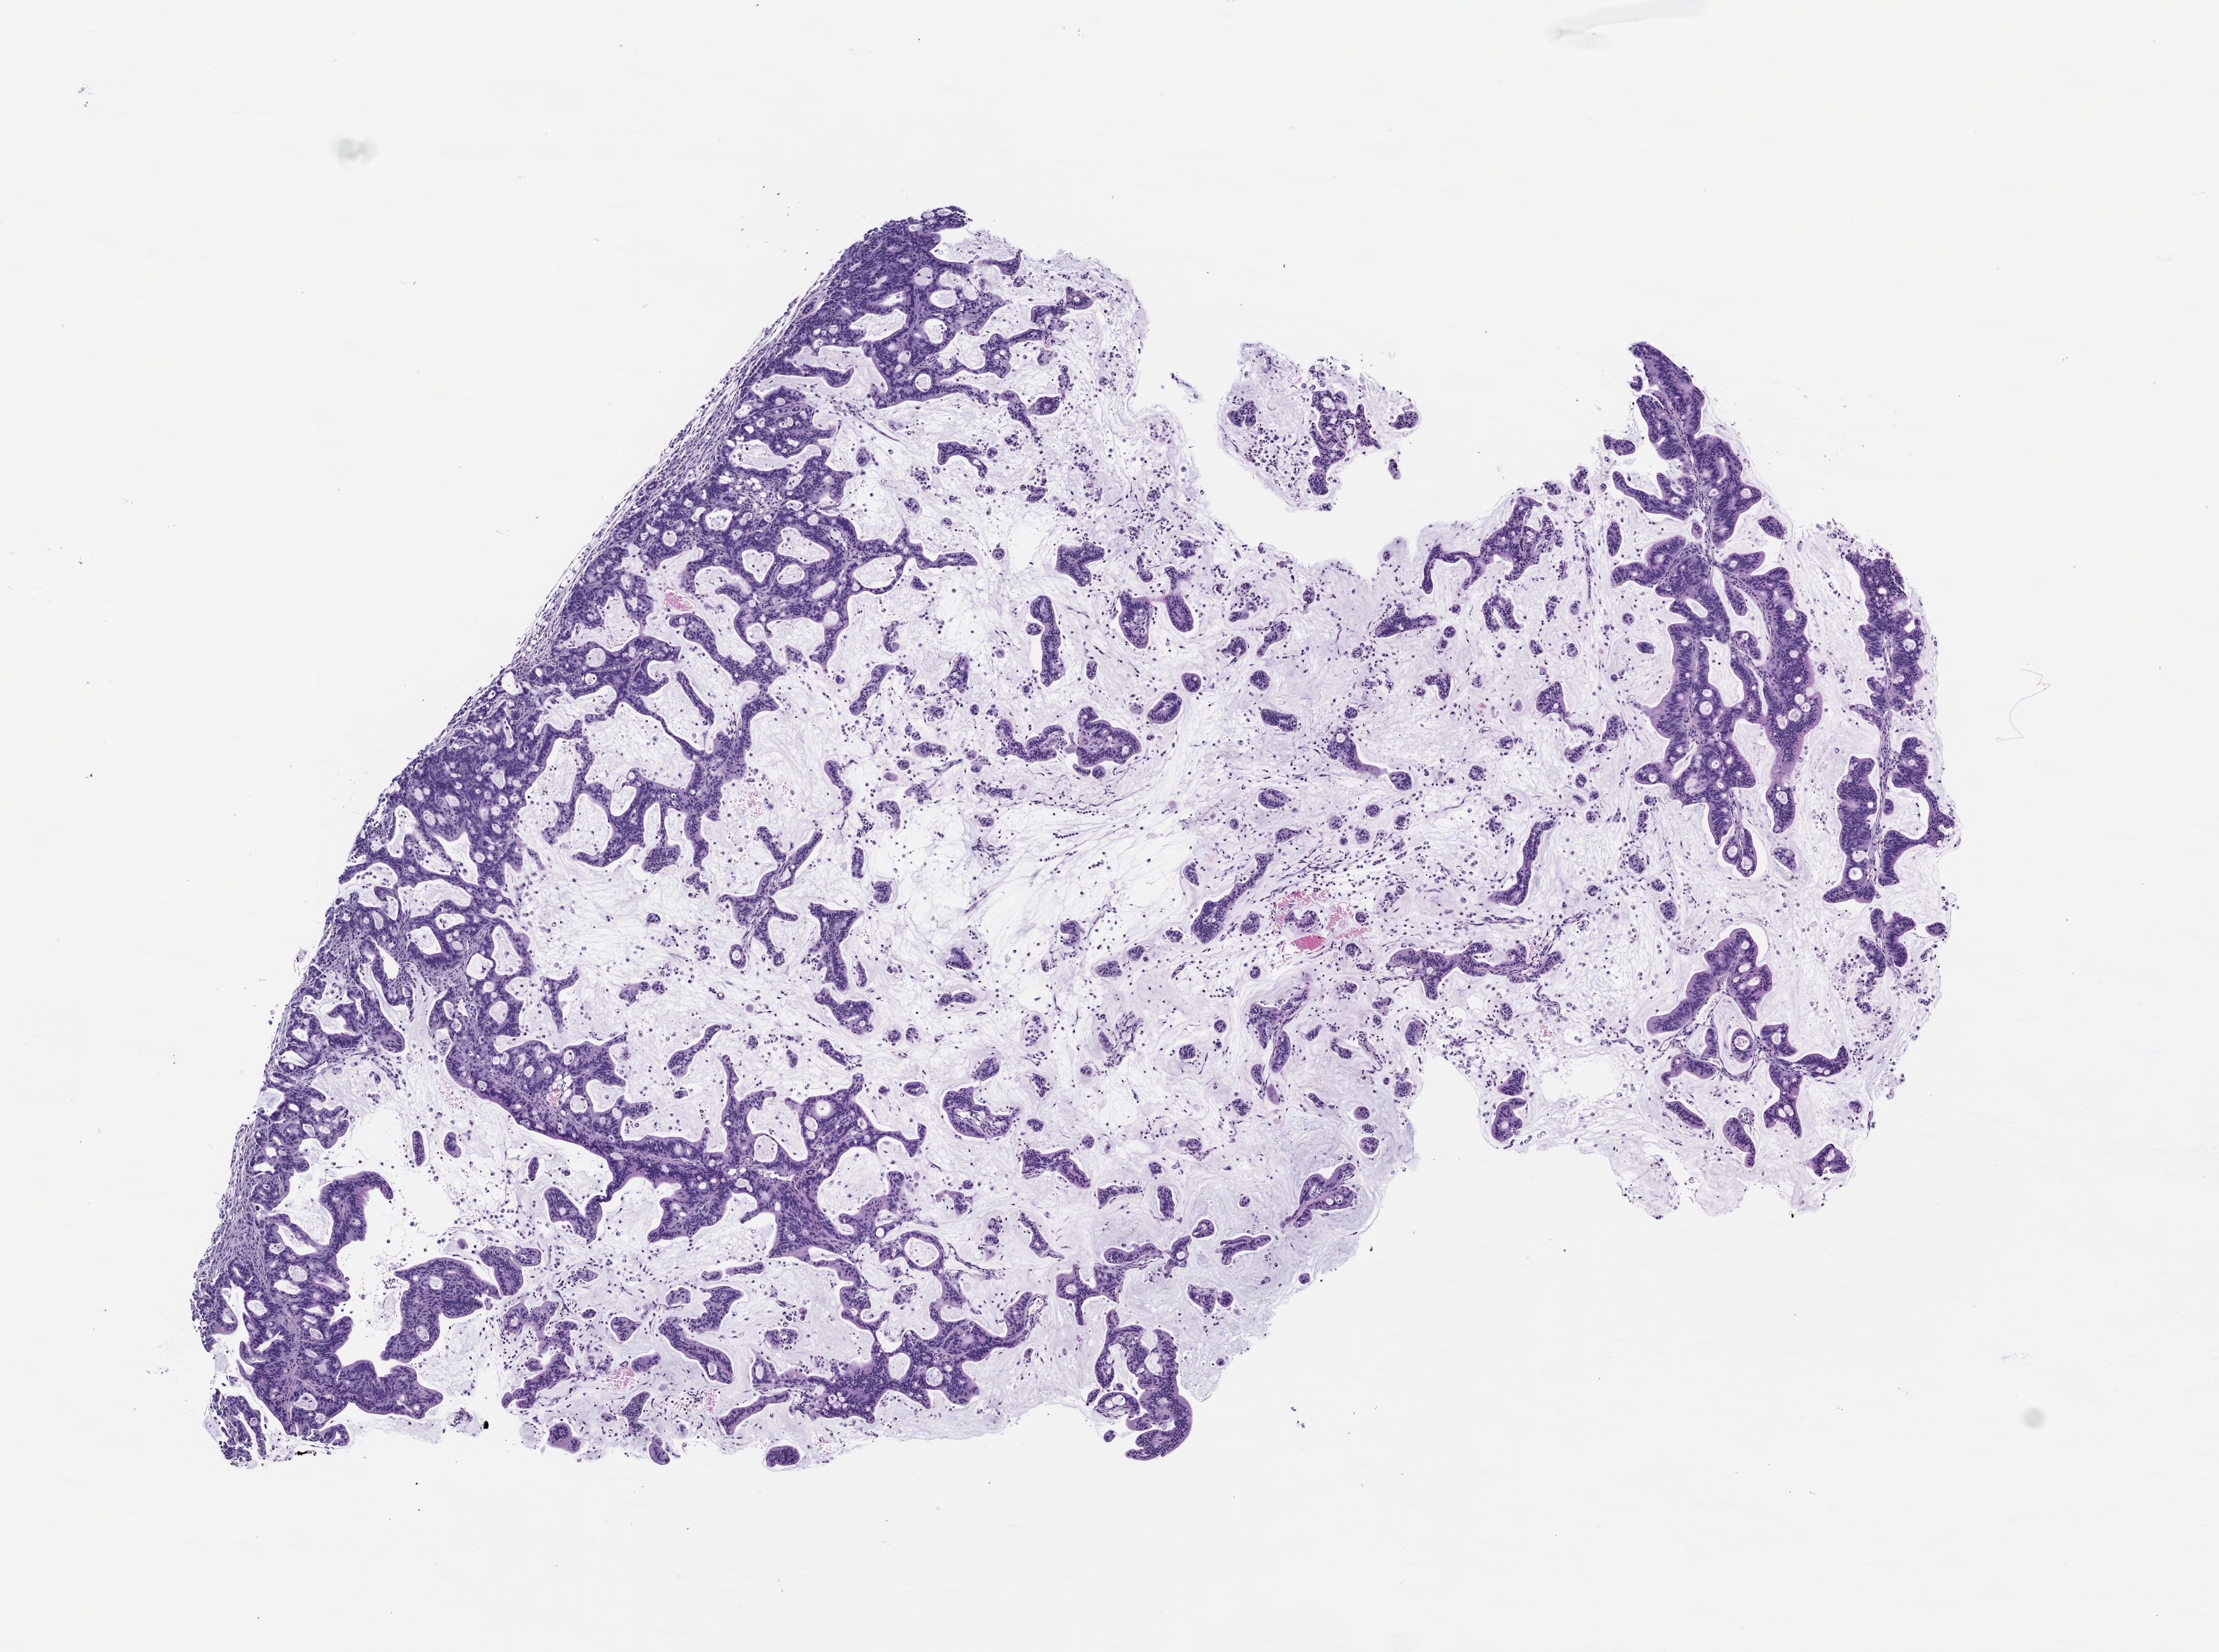
Whole-slide image, H&E: patient-derived xenograft (human tumor grown in a mouse), passage 1, shown as a low-resolution overview of the whole scanned area (about 7.0 x 5.2 mm), FFPE section, originating tumor site category: colon.
* originating patient diagnosis: Colon Adenocarcinoma